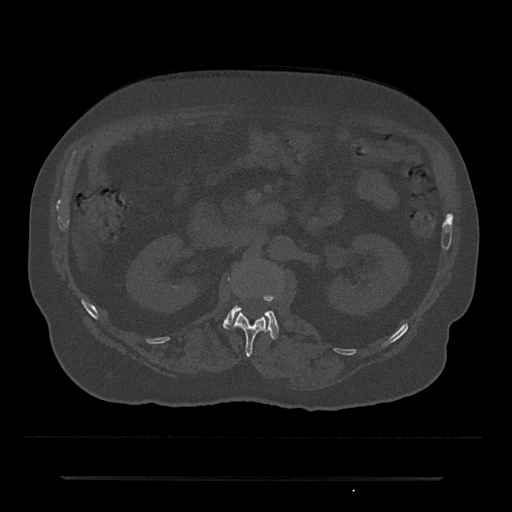
CT including the spine, one axial slice; slice 42 of 797 in the series (ordered by position); reconstruction kernel Br40s/3; bone window (W 1800 / L 400 HU); 512 × 512 image matrix, field of view 437 × 437 mm. Patient: male, 69 years. From the clinical record (not read from this slice): primary cancer: prostate.
Outlined on this slice (semi-automatically segmented with operator editing):
- L1 vertebra: bounding box (x1, y1, x2, y2) in pixels: (227, 277, 268, 357)
- L2 vertebra: (223, 296, 279, 339)